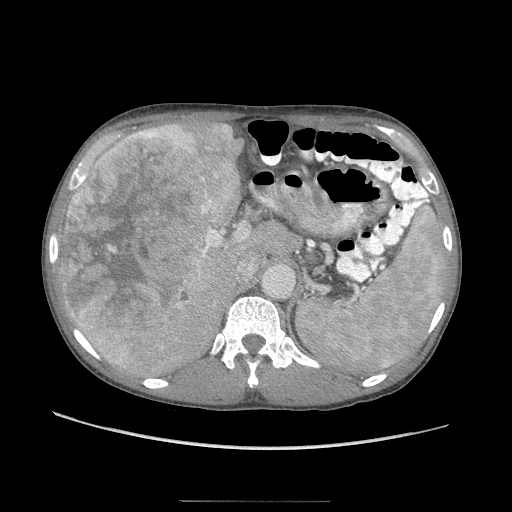
Contrast-enhanced abdominal CT (liver protocol), one axial slice; position 61 of 103 along the scan axis; 120 kVp; soft-tissue window (W 400 / L 40 HU); 2.5 mm slice thickness; 512 × 512 image matrix, field of view 380 × 380 mm. Case-level facts recorded for this patient, not image findings: diagnosis: hepatocellular carcinoma (patient treated with transarterial chemoembolisation; whether this scan precedes or follows treatment is not stated here); TNM stage (as recorded): Stage-IIIA; Child-Pugh class: A; tumour differentiation: moderately differentiated; tumour nodularity: multinodular.
Structures marked on this image (semi-automatic segmentation, software-assisted and operator-edited):
- liver parenchyma outside the tumour (the mass and vessels are separate outlines, so this box may not span the whole liver): bounding box (x1, y1, x2, y2) in pixels: (54, 116, 268, 376)
- mass: (58, 122, 242, 367)
- liver vessels: (208, 208, 265, 266)